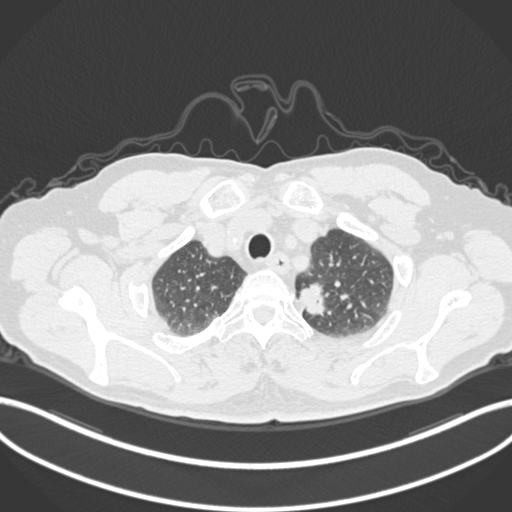
Chest CT, one axial slice. Position 278 of 306 along the scan axis. Lung window (W 1500 / L -600 HU). 1 mm slice thickness. 512 × 512 image matrix, field of view 400 × 400 mm. Male patient, age 64 years. Case-level facts recorded for this patient, not image findings: clinical TNM (as recorded): T1c N0 M0.
Outlined on this slice (rectangle marked by the reading radiologist):
- lung tumour (recorded histology: adenocarcinoma): bounding box (x1, y1, x2, y2) in pixels: (293, 278, 336, 319)